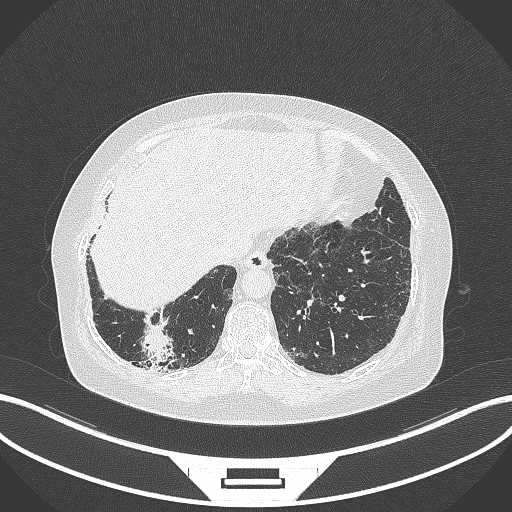
Chest CT, one axial slice; position 29 of 296 along the scan axis; reconstruction kernel B70f; 120 kVp; lung window (W 1500 / L -600 HU); 1 mm slice thickness; 512 × 512 image matrix, field of view 400 × 400 mm. Female patient, age 65 years. Case-level facts recorded for this patient, not image findings: clinical TNM (as recorded): T2b N1 M0; histopathological grade: G1.
Outlined on this slice (bounding box drawn by a radiologist):
- lung tumour (recorded histology: adenocarcinoma): bounding box (x1, y1, x2, y2) in pixels: (135, 320, 175, 367)